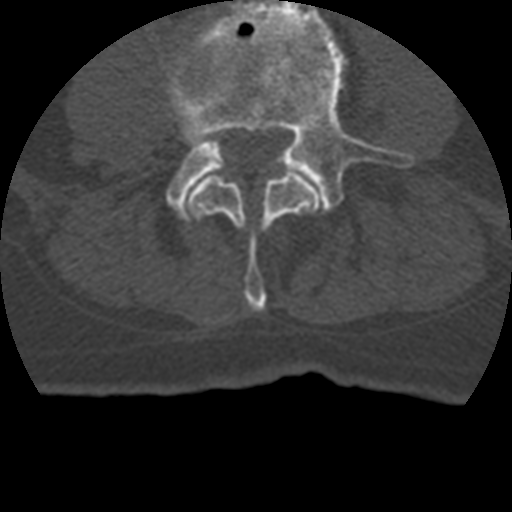
CT including the spine, one axial slice. Reconstruction kernel STANDARD. 120 kVp. Bone window (W 1800 / L 400 HU). 512 × 512 image matrix. Patient age 69 years. From the clinical record (not read from this slice): primary cancer: prostate.
Annotated regions visible in this slice (semi-automatic segmentation, software-assisted and operator-edited):
- L3 vertebra: bounding box <189,172,321,312> (left, top, right, bottom; pixels)
- L4 vertebra: <164,0,418,220>